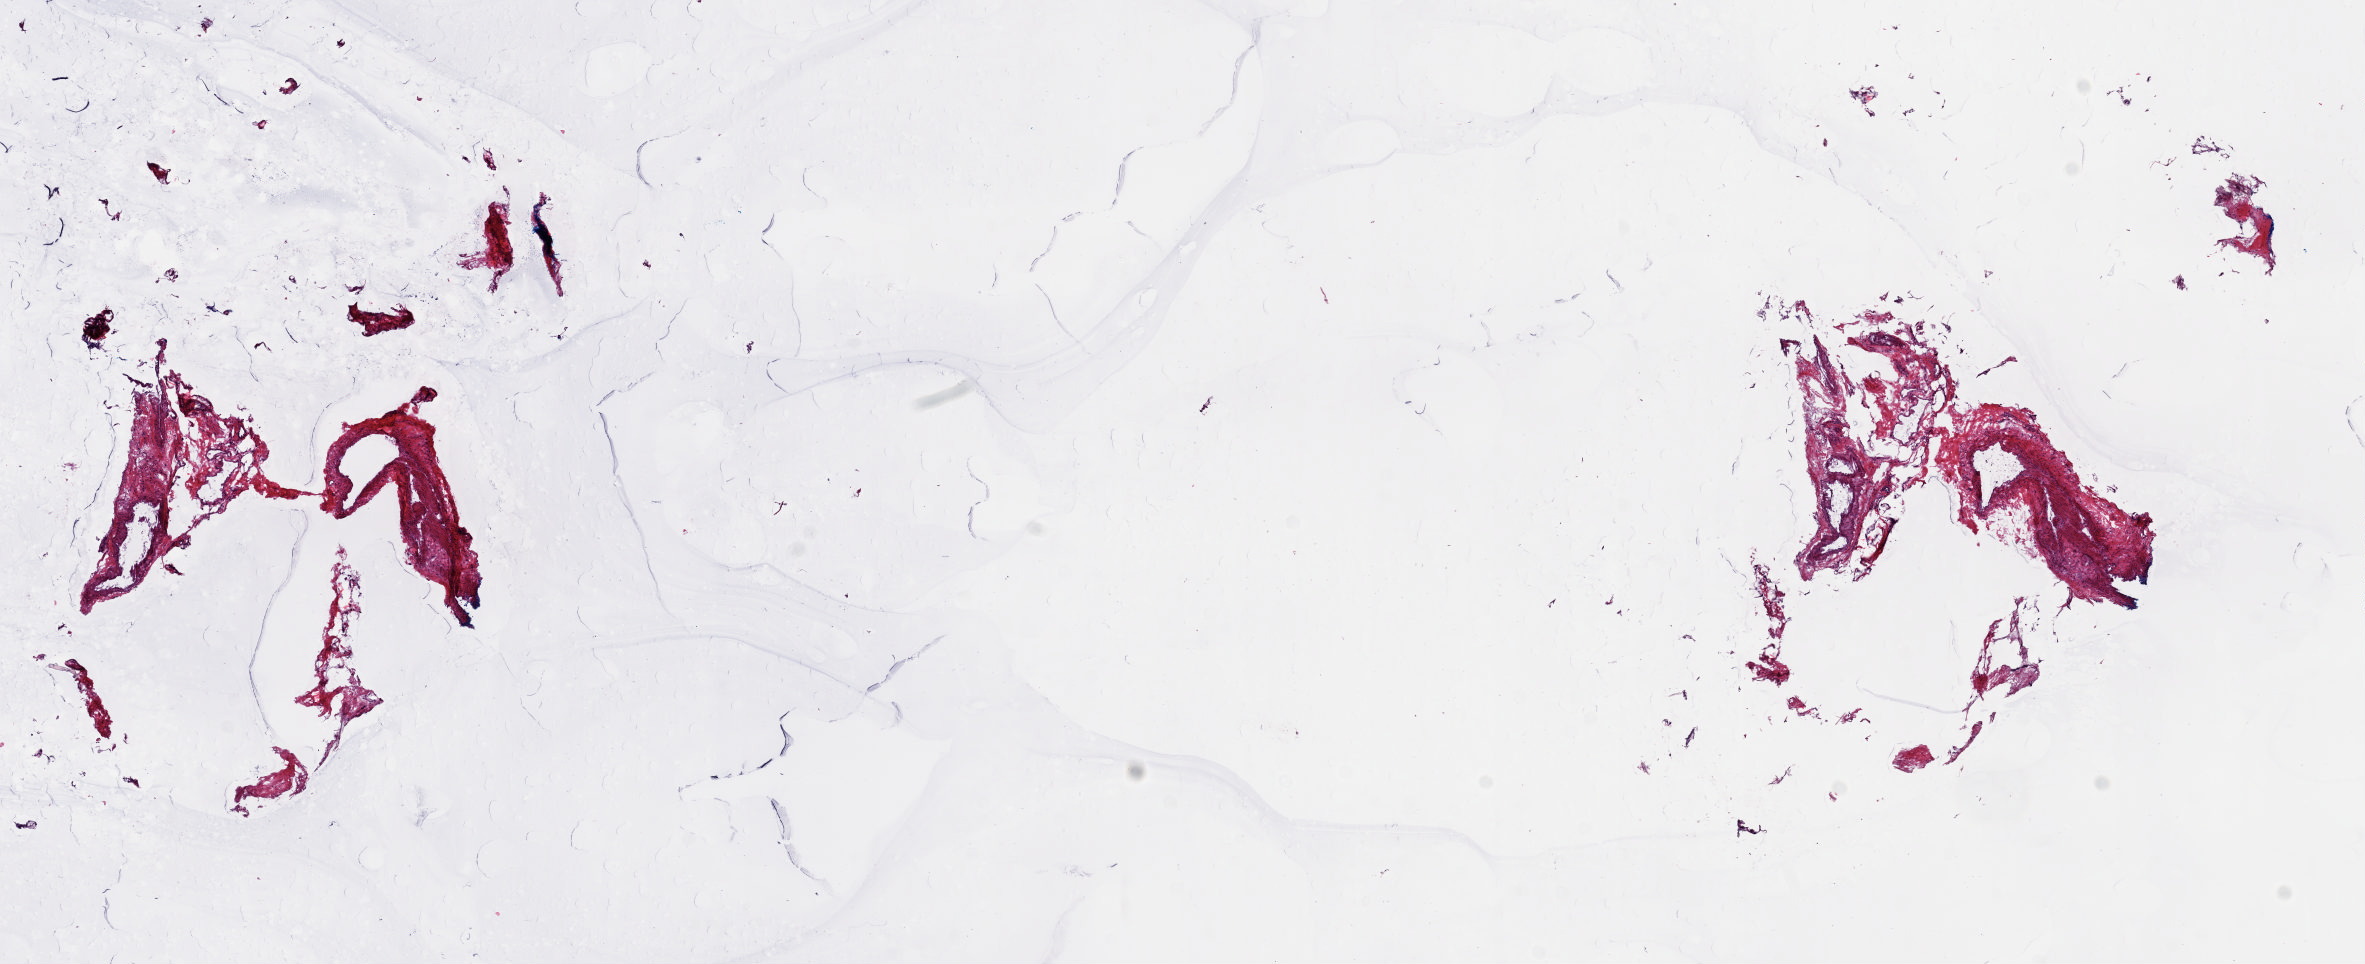
Hematoxylin and eosin (H&E) stained whole-slide image — a low-resolution overview of the entire scanned area, about 18.6 x 7.6 mm (slide scanned at 20x); frozen section from the top of the tissue portion; solid tissue normal (non-tumour tissue) sample from the breast. Female, age 79 years at initial diagnosis. Pathologist review of this section (percent, as recorded): tumour cells 0%, tumour nuclei 0%, normal cells 0%, stromal cells 100%, necrosis 0%. Infiltration values recorded for this section: lymphocyte infiltration 0%, monocyte infiltration 0%, neutrophil infiltration 0%.
- this section: solid tissue normal sample (biorepository sample class)
- patient diagnosis: Pleomorphic carcinoma